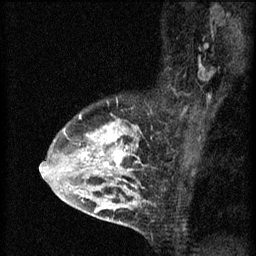
Breast MRI (dynamic contrast-enhanced), one sagittal slice; position 43 of 60 along the scan axis; 3 images stored at this slice position (order not interpretable as contrast timing); 1.5 T; TE 4.2 ms, TR 8.2 ms; 256 × 256 image matrix, field of view 180 × 180 mm. Patient: female, 45 years.
Structures marked on this image (semi-automatically segmented with operator editing):
- analysis volume of interest (the breast-tissue region the enhancement analysis was run in; not a lesion): bounding box <54,108,145,217> (left, top, right, bottom; pixels)
- tumour enhancement mask (voxels above the 70 % enhancement threshold inside the analysis volume of interest): <60,116,139,213>